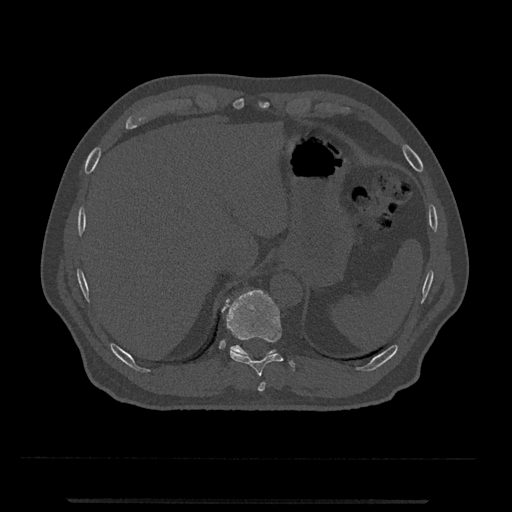
CT including the spine, one axial slice. Position 506 of 797 along the scan axis. Bone window (W 1800 / L 400 HU). 512 × 512 image matrix. Male patient, age 63 years. Case-level facts recorded for this patient, not image findings: primary cancer: prostate.
Outlined on this slice (semi-automatically segmented with operator editing):
- T10 vertebra: bounding box (x1, y1, x2, y2) in pixels: (222, 290, 295, 377)
- T11 vertebra: (230, 345, 277, 357)
- T9 vertebra: (258, 382, 265, 392)